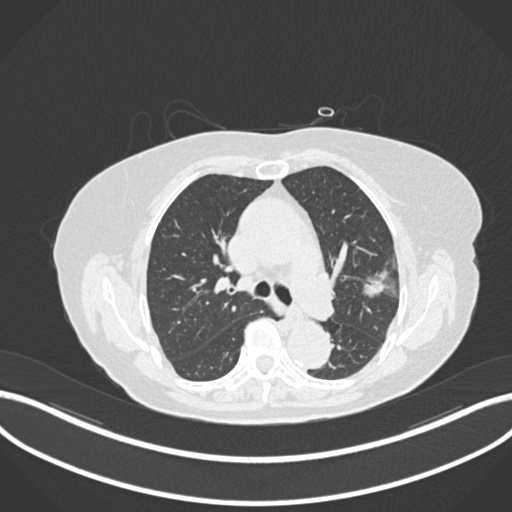
Chest CT, one axial slice; slice 104 of 168 in the series (ordered by position); 120 kVp; lung window (W 1500 / L -600 HU); 512 × 512 image matrix, field of view 400 × 400 mm. Patient: female, 75 years. From the clinical record (not read from this slice): clinical TNM (as recorded): T1c N0 M0.
Annotated regions visible in this slice (bounding box drawn by a radiologist):
- lung tumour (recorded histology: adenocarcinoma): box from (x=360, y=268) to (x=386, y=301) px